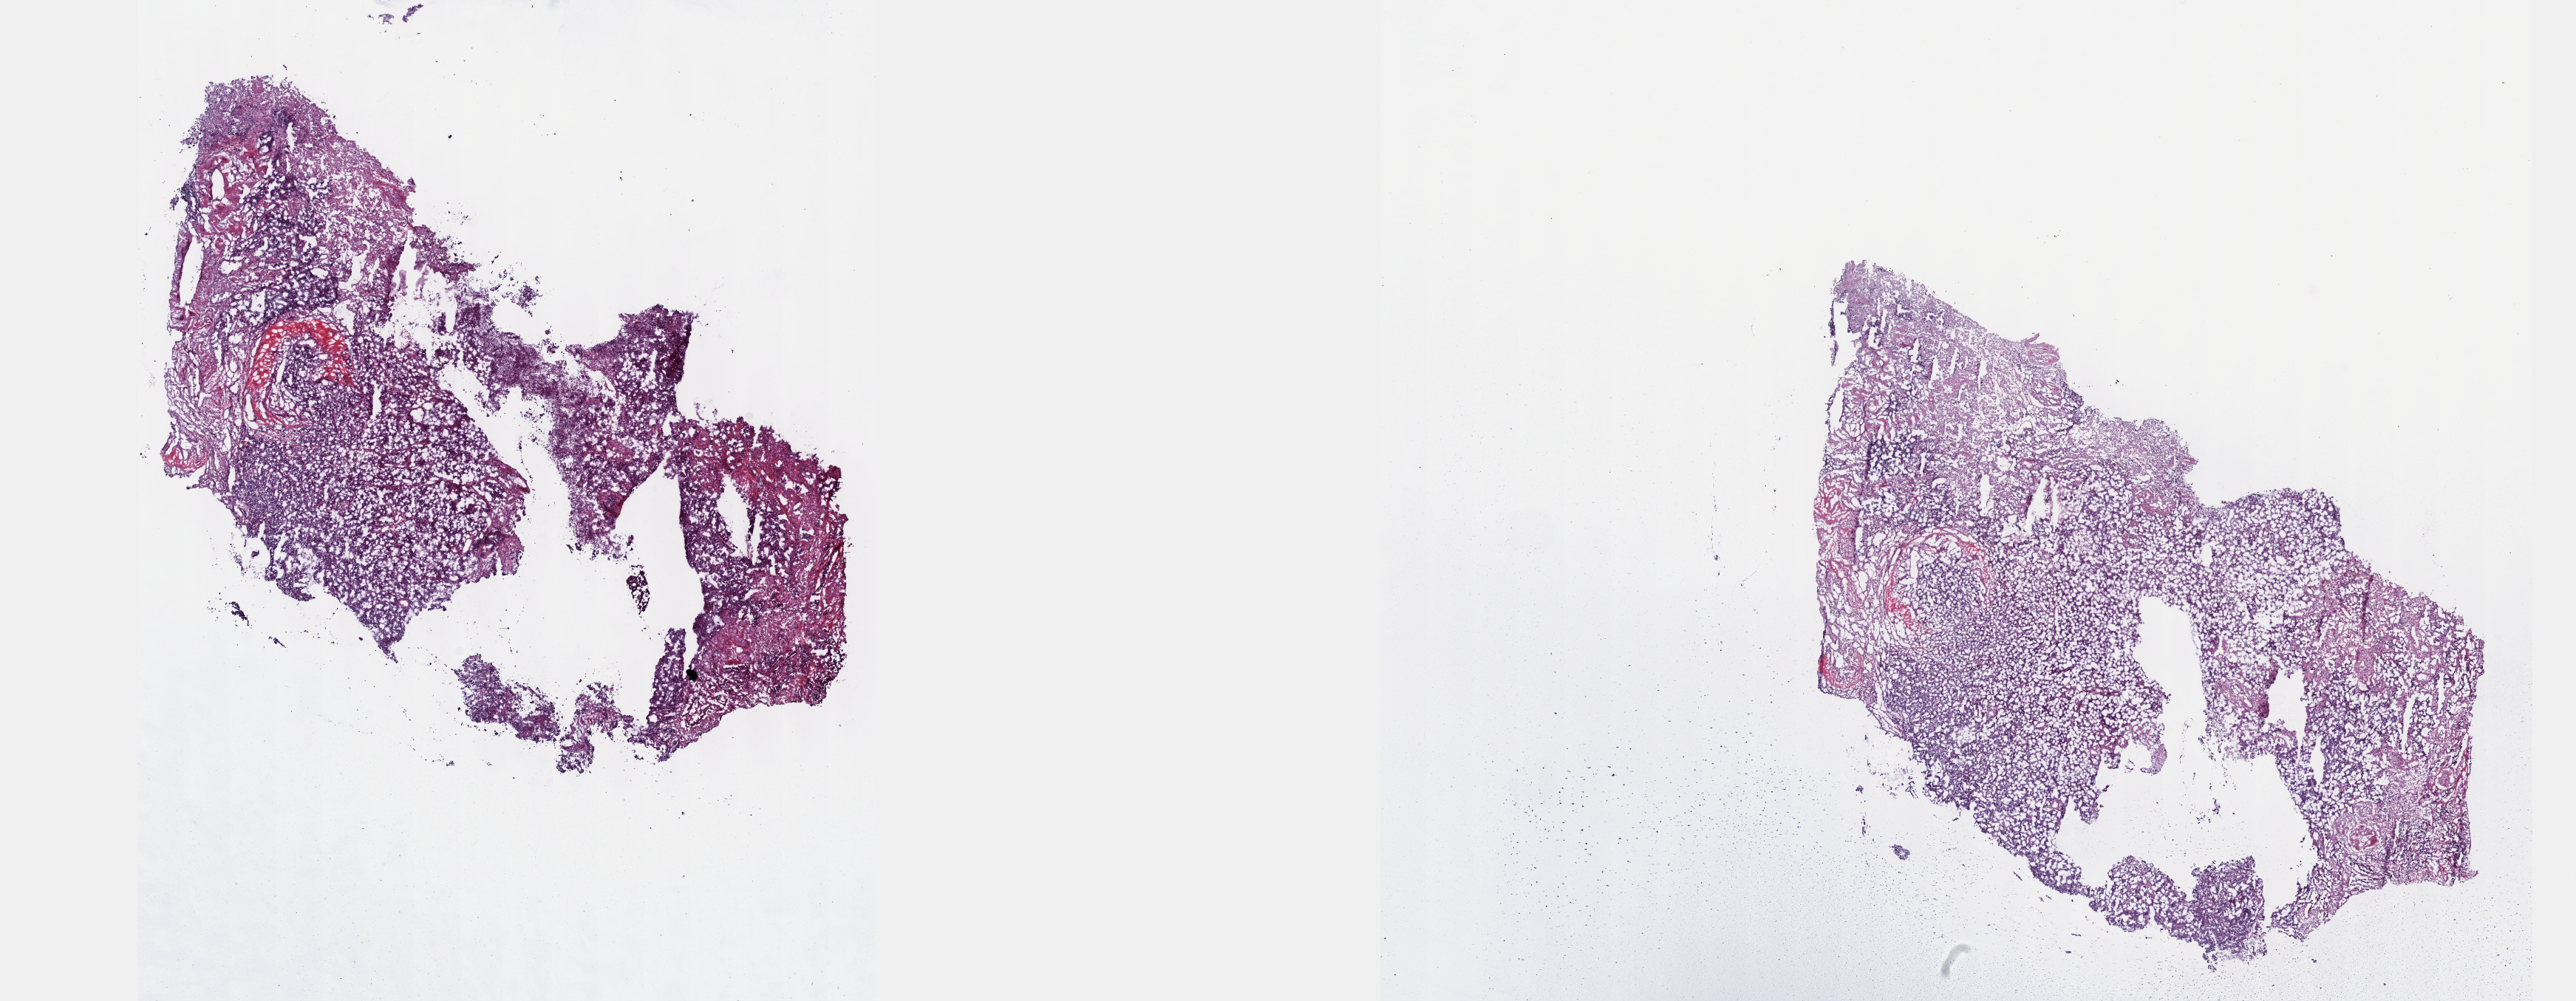
Whole-slide histology image, H&E, a low-resolution overview of the entire scanned area, about 28.2 x 10.9 mm (from a 40x scan); frozen section from the top of the tissue portion; lung, primary tumour sample. Female, age 63 years at initial diagnosis. Slide review estimates, as recorded: tumour cells 80%, tumour nuclei 90%, normal cells 0%, stromal cells 0%, necrosis 20%. Infiltration values recorded for this section: lymphocyte infiltration 0%, monocyte infiltration 0%, neutrophil infiltration 0%.
• AJCC pathologic stage: II (7th edition)
• laterality: left
• pathologic diagnosis: Adenocarcinoma with mixed subtypes (lower lobe, lung)